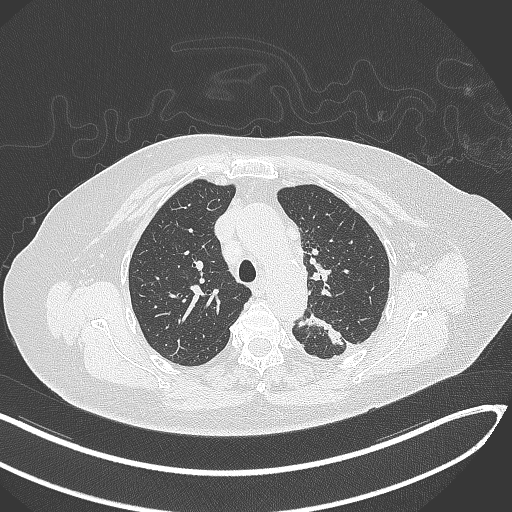
Chest CT, one axial slice; position 227 of 270 along the scan axis; 120 kVp; lung window (W 1500 / L -600 HU); 1 mm slice thickness; 512 × 512 image matrix. Patient: female, 76 years. Case-level facts recorded for this patient, not image findings: clinical TNM (as recorded): T1c N0 M0.
Annotated regions visible in this slice (rectangle marked by the reading radiologist):
- lung tumour (recorded histology: adenocarcinoma): bounding box <290,311,344,350> (left, top, right, bottom; pixels)